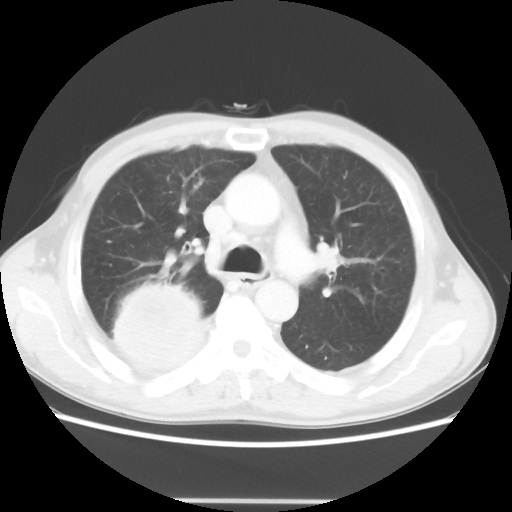
Chest CT, one axial slice; slice 33 of 48 in the series (ordered by position); reconstruction kernel STANDARD; lung window (W 1500 / L -600 HU); 5 mm slice thickness; 512 × 512 image matrix. Patient: male, 66 years. From the clinical record (not read from this slice): clinical TNM (as recorded): T4 N1 M1.
Annotated regions visible in this slice (bounding box drawn by a radiologist):
- lung tumour (recorded histology: small cell carcinoma): box from (x=103, y=277) to (x=213, y=384) px